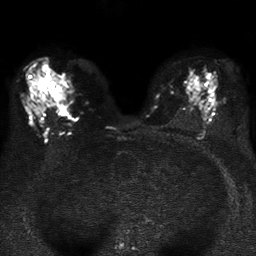
Breast MRI, one axial slice; slice 20 of 37 in the series (ordered by position); diffusion-weighted series; image 2 of 4 stored at this slice position (different b-values; order by instance number); 1.5 T; 5 mm slice thickness; 256 × 256 image matrix, field of view 320 × 320 mm. Female patient.
Structures marked on this image (manually delineated by an expert):
- tumour on diffusion-weighted imaging: bounding box (x1, y1, x2, y2) in pixels: (52, 85, 64, 100)